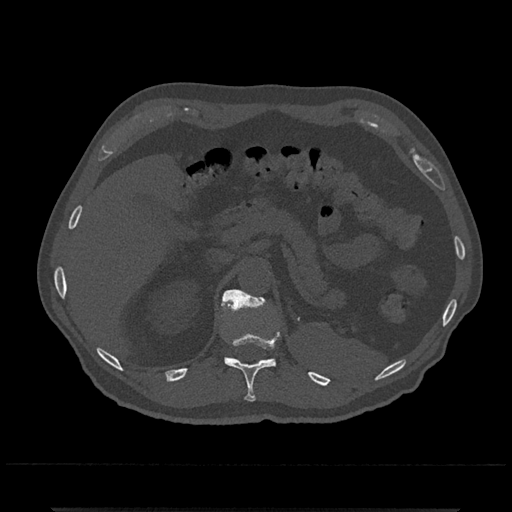
CT including the spine, one axial slice; position 472 of 797 along the scan axis; bone window (W 1800 / L 400 HU); 0.5 mm slice thickness; 512 × 512 image matrix, field of view 393 × 393 mm. Patient: male, 67 years. From the clinical record (not read from this slice): primary cancer: prostate.
Outlined on this slice (semi-automatically segmented with operator editing):
- T11 vertebra: bounding box [x1, y1, x2, y2] px = [221, 302, 279, 402]
- T12 vertebra: [222, 289, 271, 359]